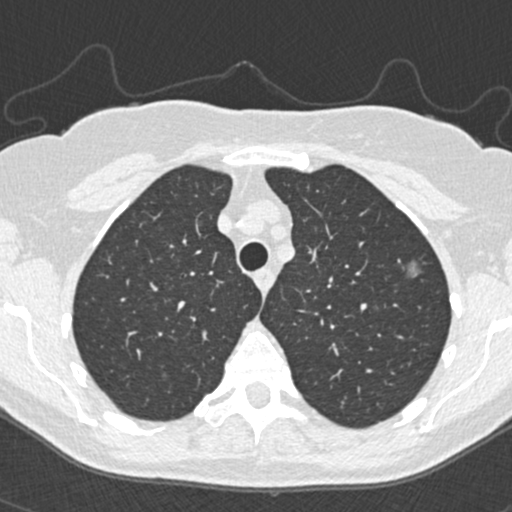
Low-dose screening chest CT, one axial slice; position 282 of 350 along the scan axis; reconstruction kernel B30f; lung window (W 1500 / L -600 HU); 1 mm slice thickness; 512 × 512 image matrix.
Annotated regions visible in this slice (outlined manually by an expert reader):
- lesion 3 (tumor, upper lobe of left lung): bounding box <407,263,419,278> (left, top, right, bottom; pixels)